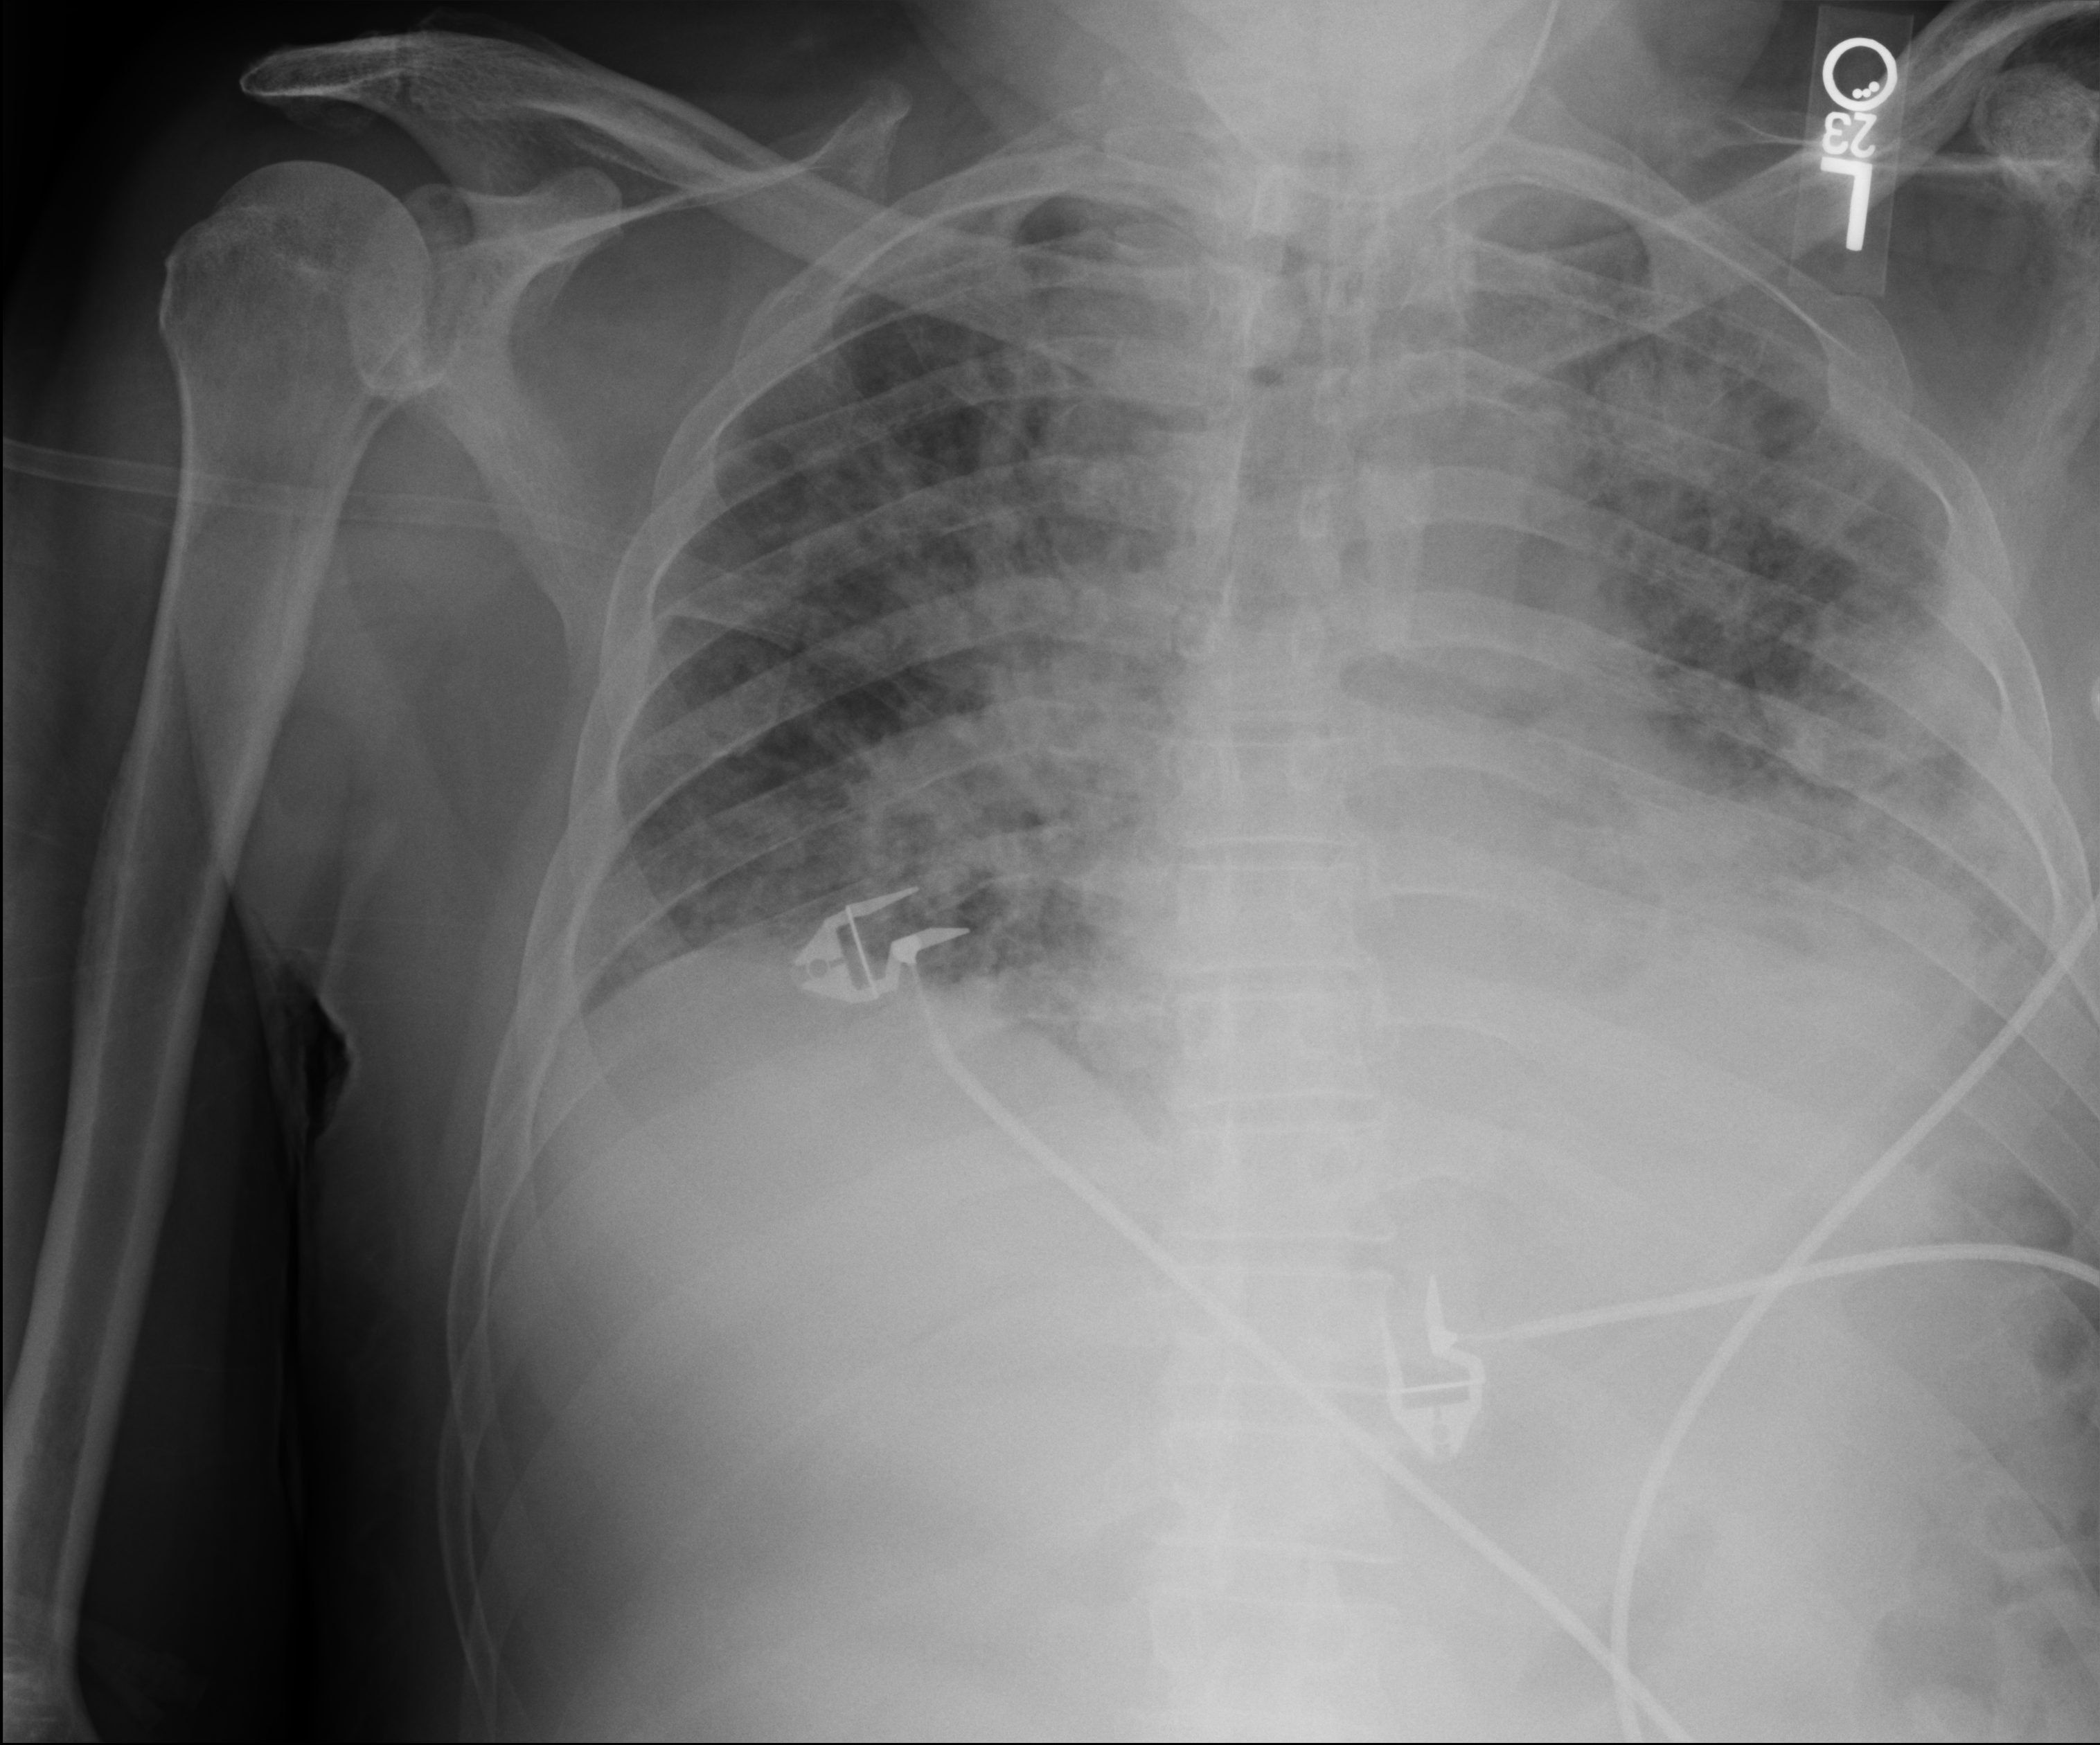
Chest X-ray (portable). Male patient hospitalised with COVID-19, age 60–74 years.
Hospital-stay facts (about this admission, not read from this image; timing relative to this image not recorded): admitted to intensive care during this hospital stay: no.